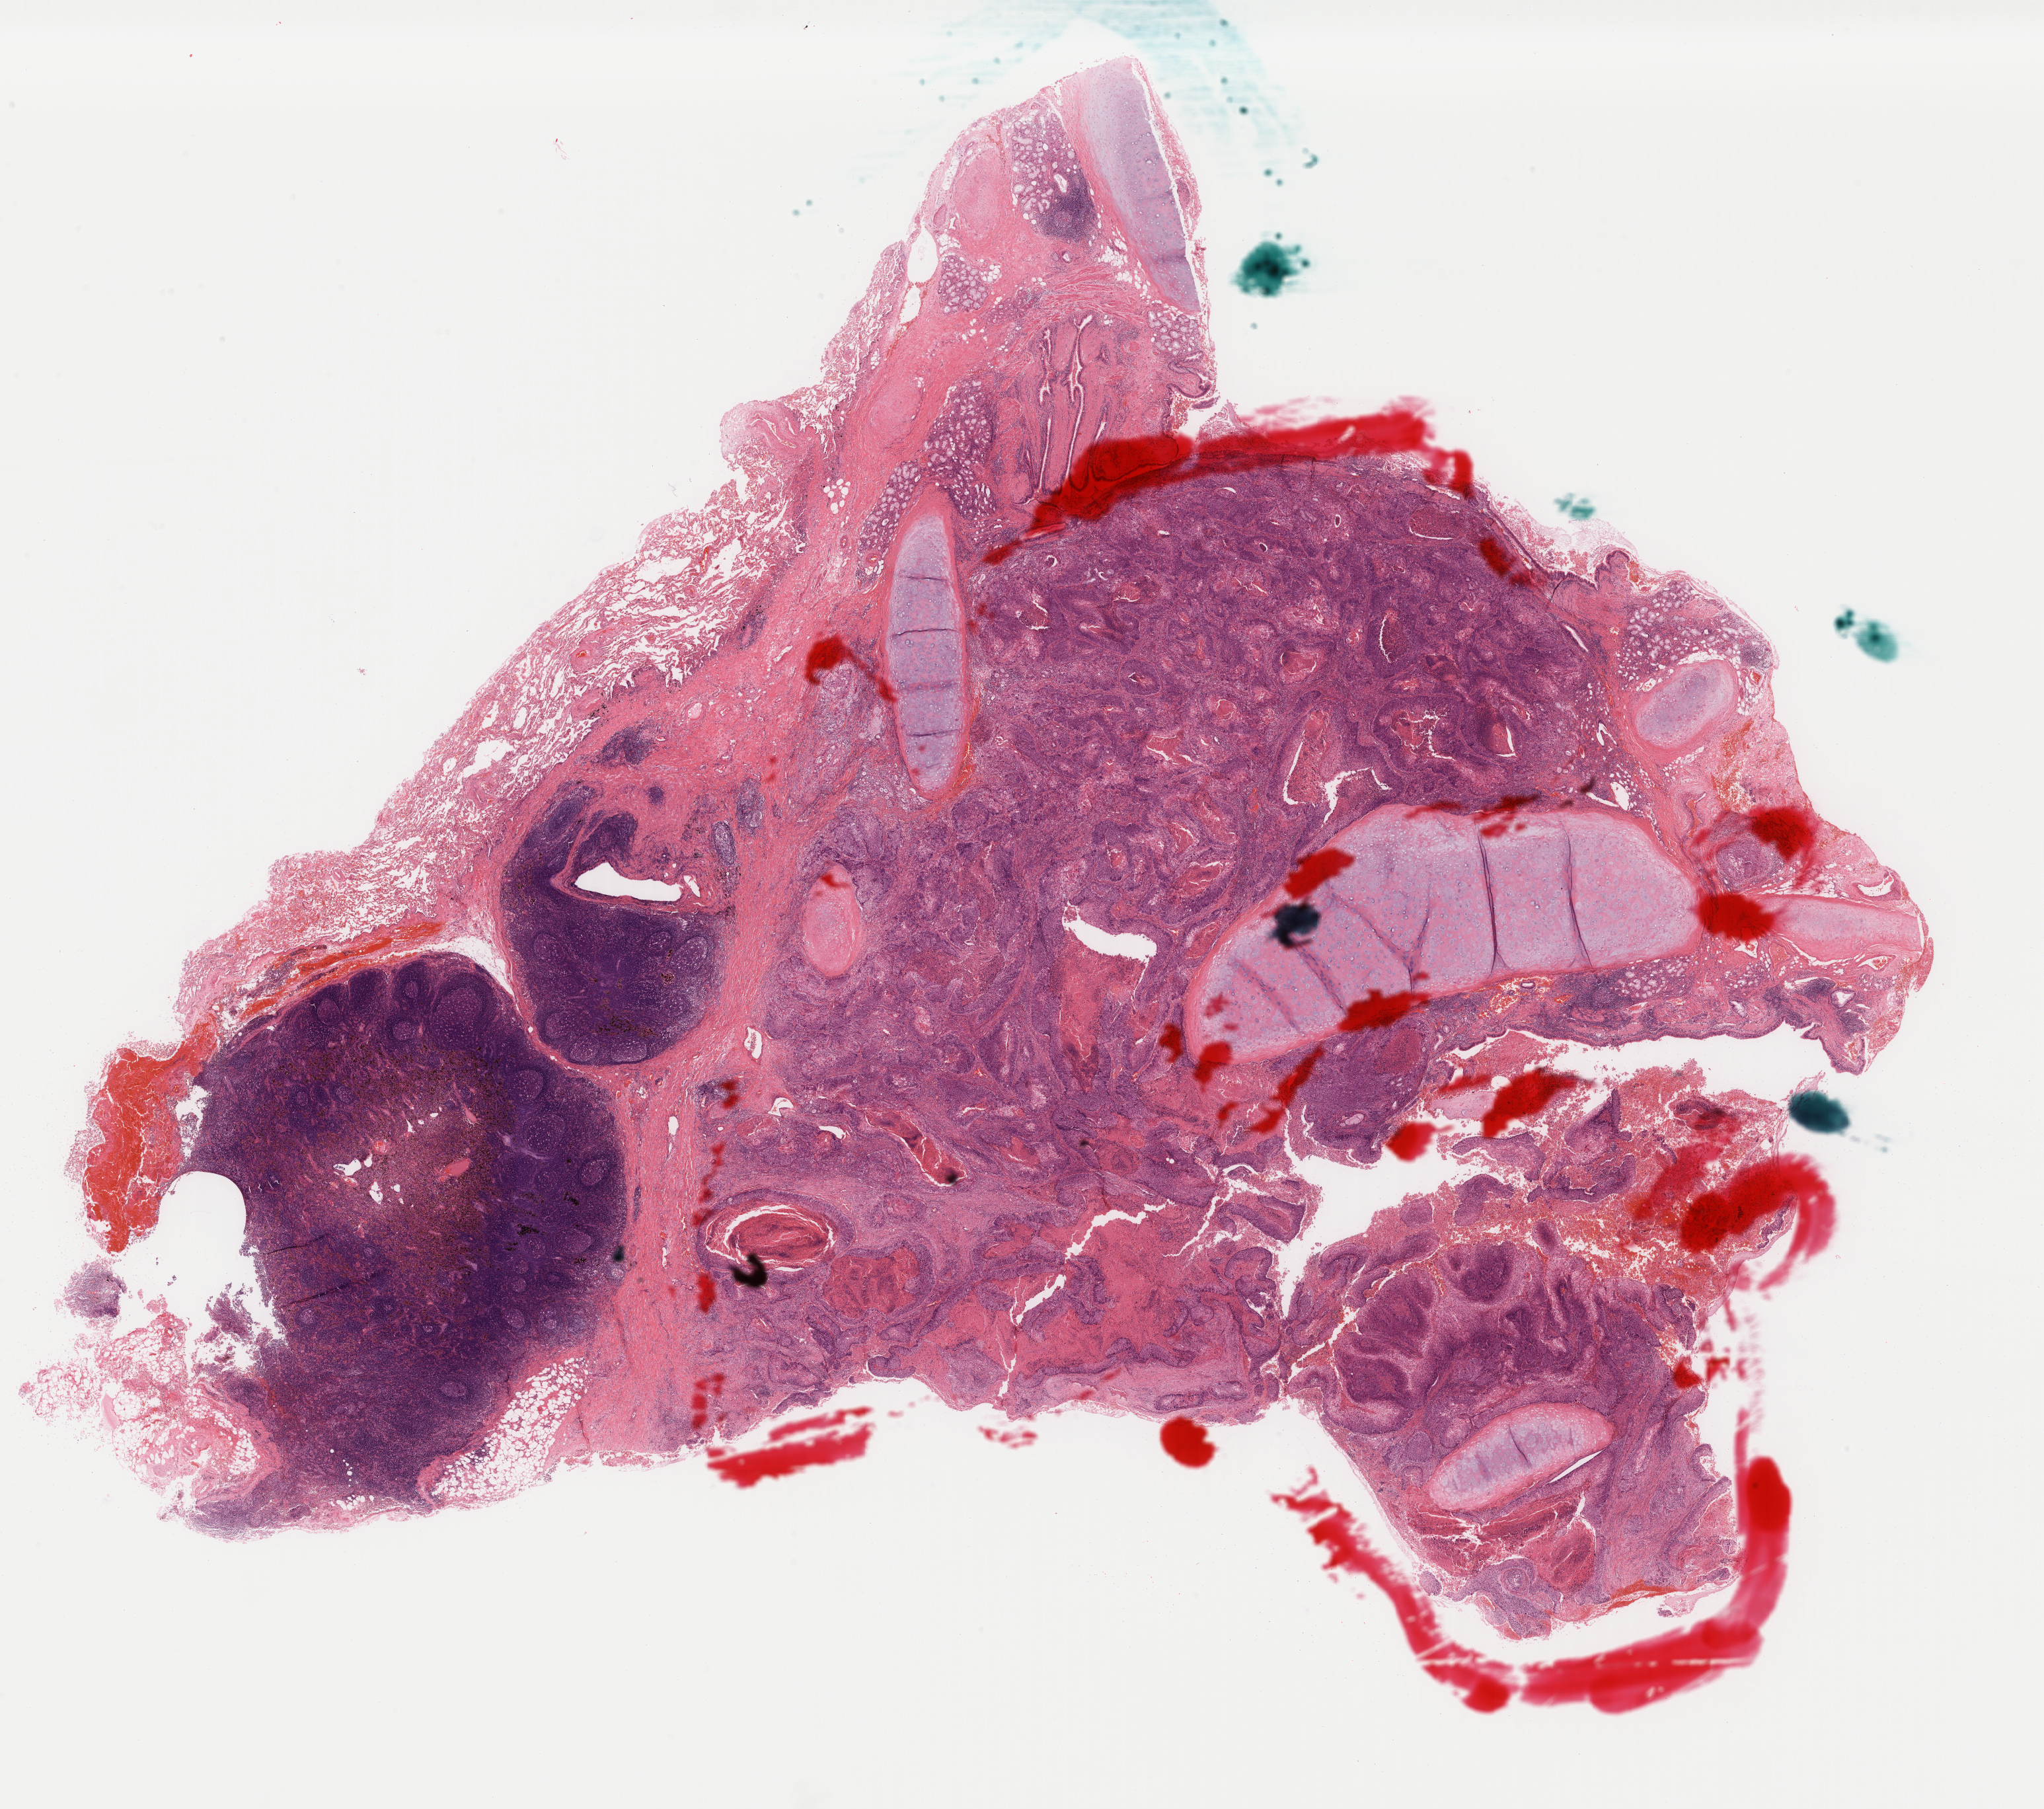
Digitized H&E-stained tissue section (whole slide) — shown as a low-resolution overview of the whole scanned area (about 24.6 x 21.7 mm), formalin-fixed paraffin-embedded (FFPE) diagnostic section, primary tumour sample from the lung. Male patient; age at initial diagnosis 61 years.
AJCC pathologic stage: IB (7th edition). Histologic diagnosis: Squamous cell carcinoma, large cell, nonkeratinizing, NOS (lower lobe, lung). TNM: T2a N0 M0.